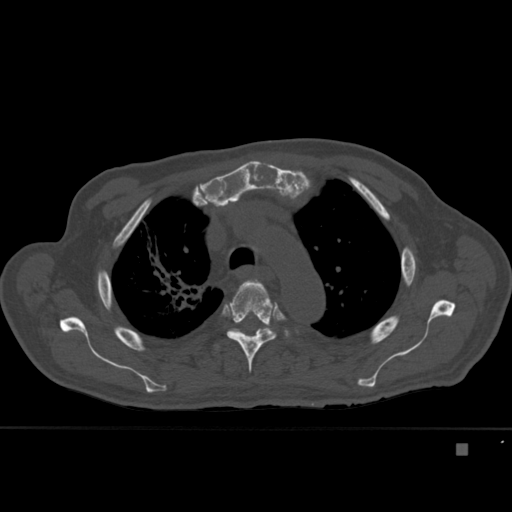
CT including the spine, one axial slice. Position 320 of 451 along the scan axis. Bone window (W 1800 / L 400 HU). 1.5 mm slice thickness. 512 × 512 image matrix. Patient: male, 75 years. Case-level facts recorded for this patient, not image findings: primary cancer: prostate.
Outlined on this slice (semi-automatic segmentation, software-assisted and operator-edited):
- T4 vertebra: bounding box <227,279,289,373> (left, top, right, bottom; pixels)
- T5 vertebra: <218,327,269,347>